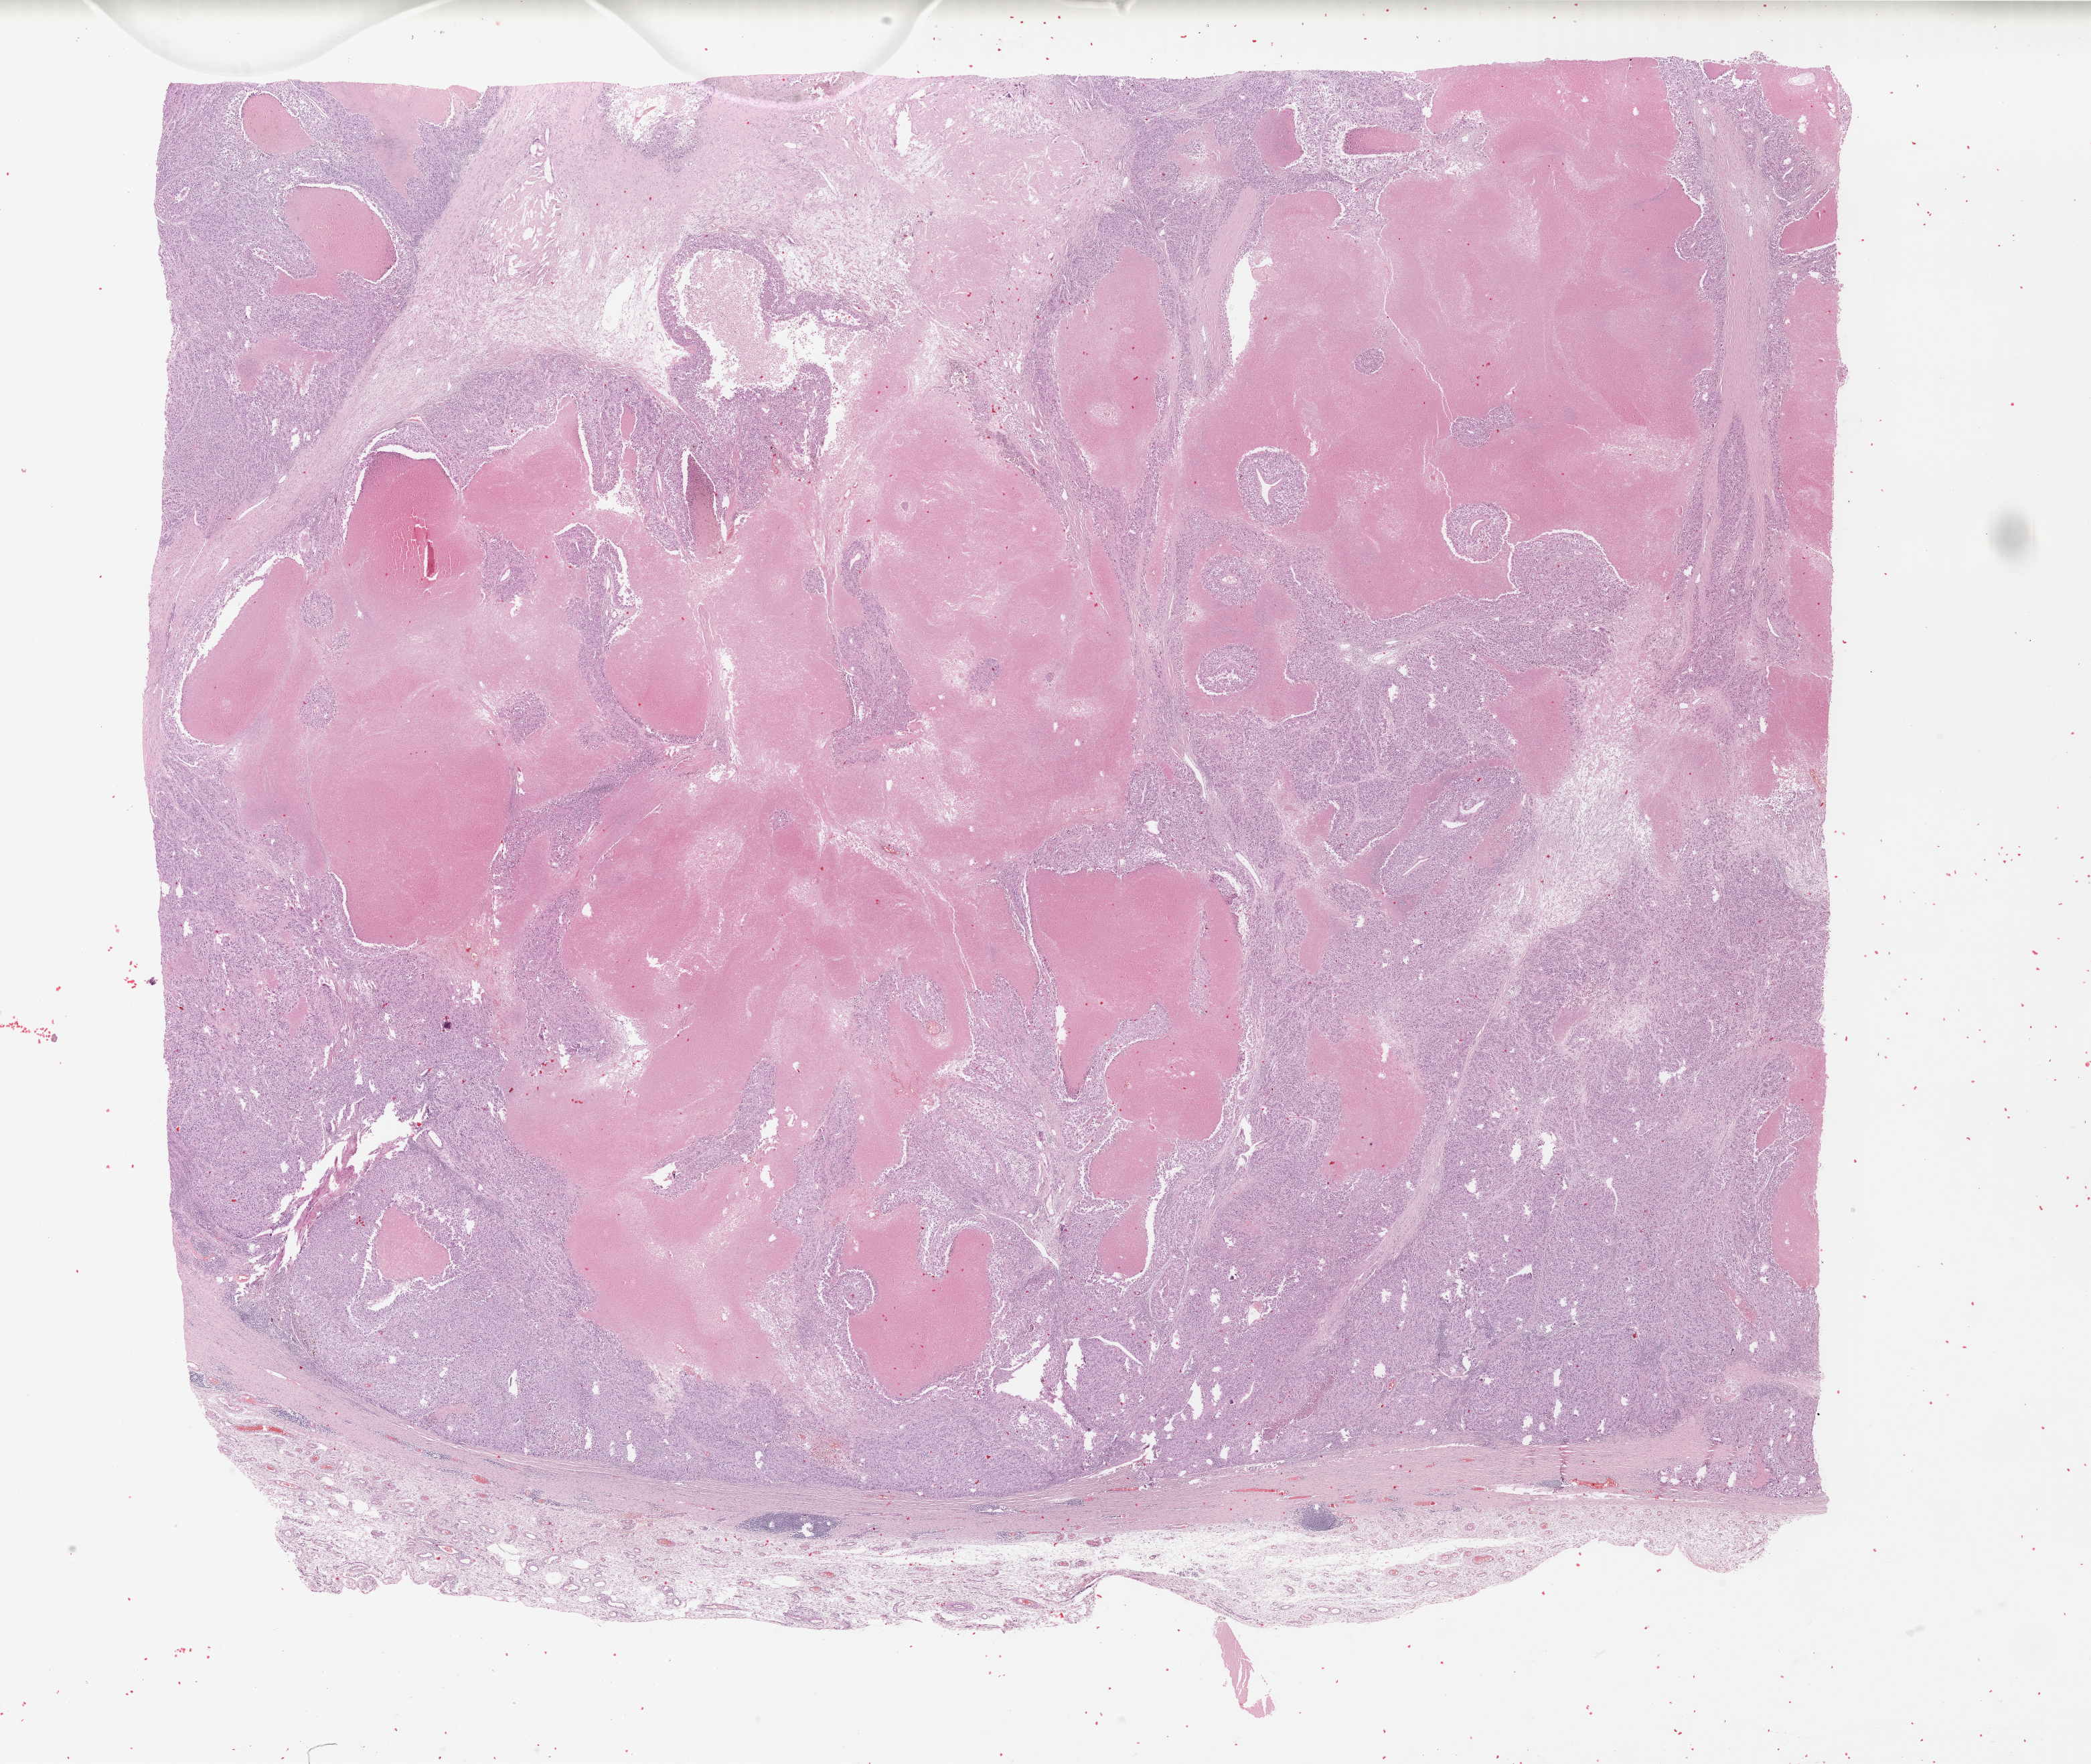
Digitized H&E tissue section (whole slide), whole scanned area (about 24.8 x 20.9 mm, acquisition: 40x scan) shown as a low-resolution overview, formalin-fixed paraffin-embedded (FFPE) diagnostic section, primary tumour sample from the skin. Male patient; age at initial diagnosis 40 years.
Histologic diagnosis: Malignant melanoma, NOS.